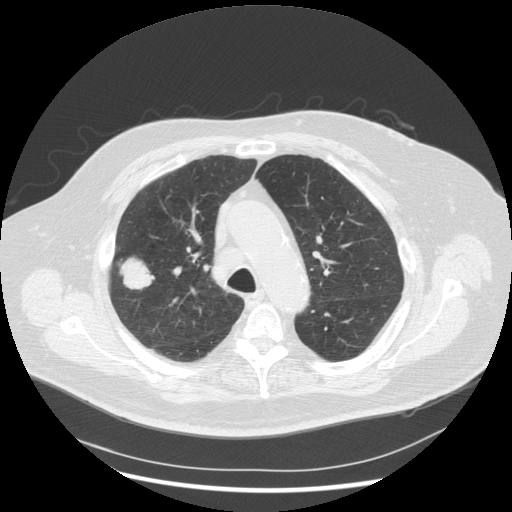
Low-dose screening chest CT, one axial slice; position 199 of 263 along the scan axis; reconstruction kernel STANDARD; 120 kVp; lung window (W 1500 / L -600 HU); 2.5 mm slice thickness; 512 × 512 image matrix, field of view 400 × 400 mm.
Outlined on this slice (expert manual segmentation):
- lesion 1 (tumor, upper lobe of right lung): bounding box [x1, y1, x2, y2] px = [120, 258, 155, 289]